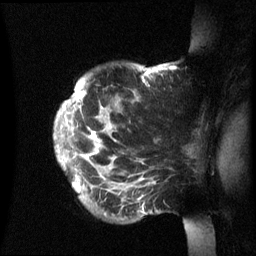
Breast MRI (dynamic contrast-enhanced), one sagittal slice. Slice 50 of 60 in the series (ordered by position). Dynamic contrast-enhanced series, image 2 of 3 at this slice position (ordered by acquisition). 1.5 T. TE 4.2 ms, TR 8.4 ms. 2.4 mm slice thickness. 256 × 256 image matrix, field of view 230 × 230 mm. Patient: female, 48 years.
Outlined on this slice (semi-automatic segmentation, software-assisted and operator-edited):
- analysis volume of interest (the breast-tissue region the enhancement analysis was run in; not a lesion): bounding box [x1, y1, x2, y2] px = [55, 64, 202, 236]
- tumour enhancement mask (voxels above the 70 % enhancement threshold inside the analysis volume of interest): [56, 67, 163, 180]